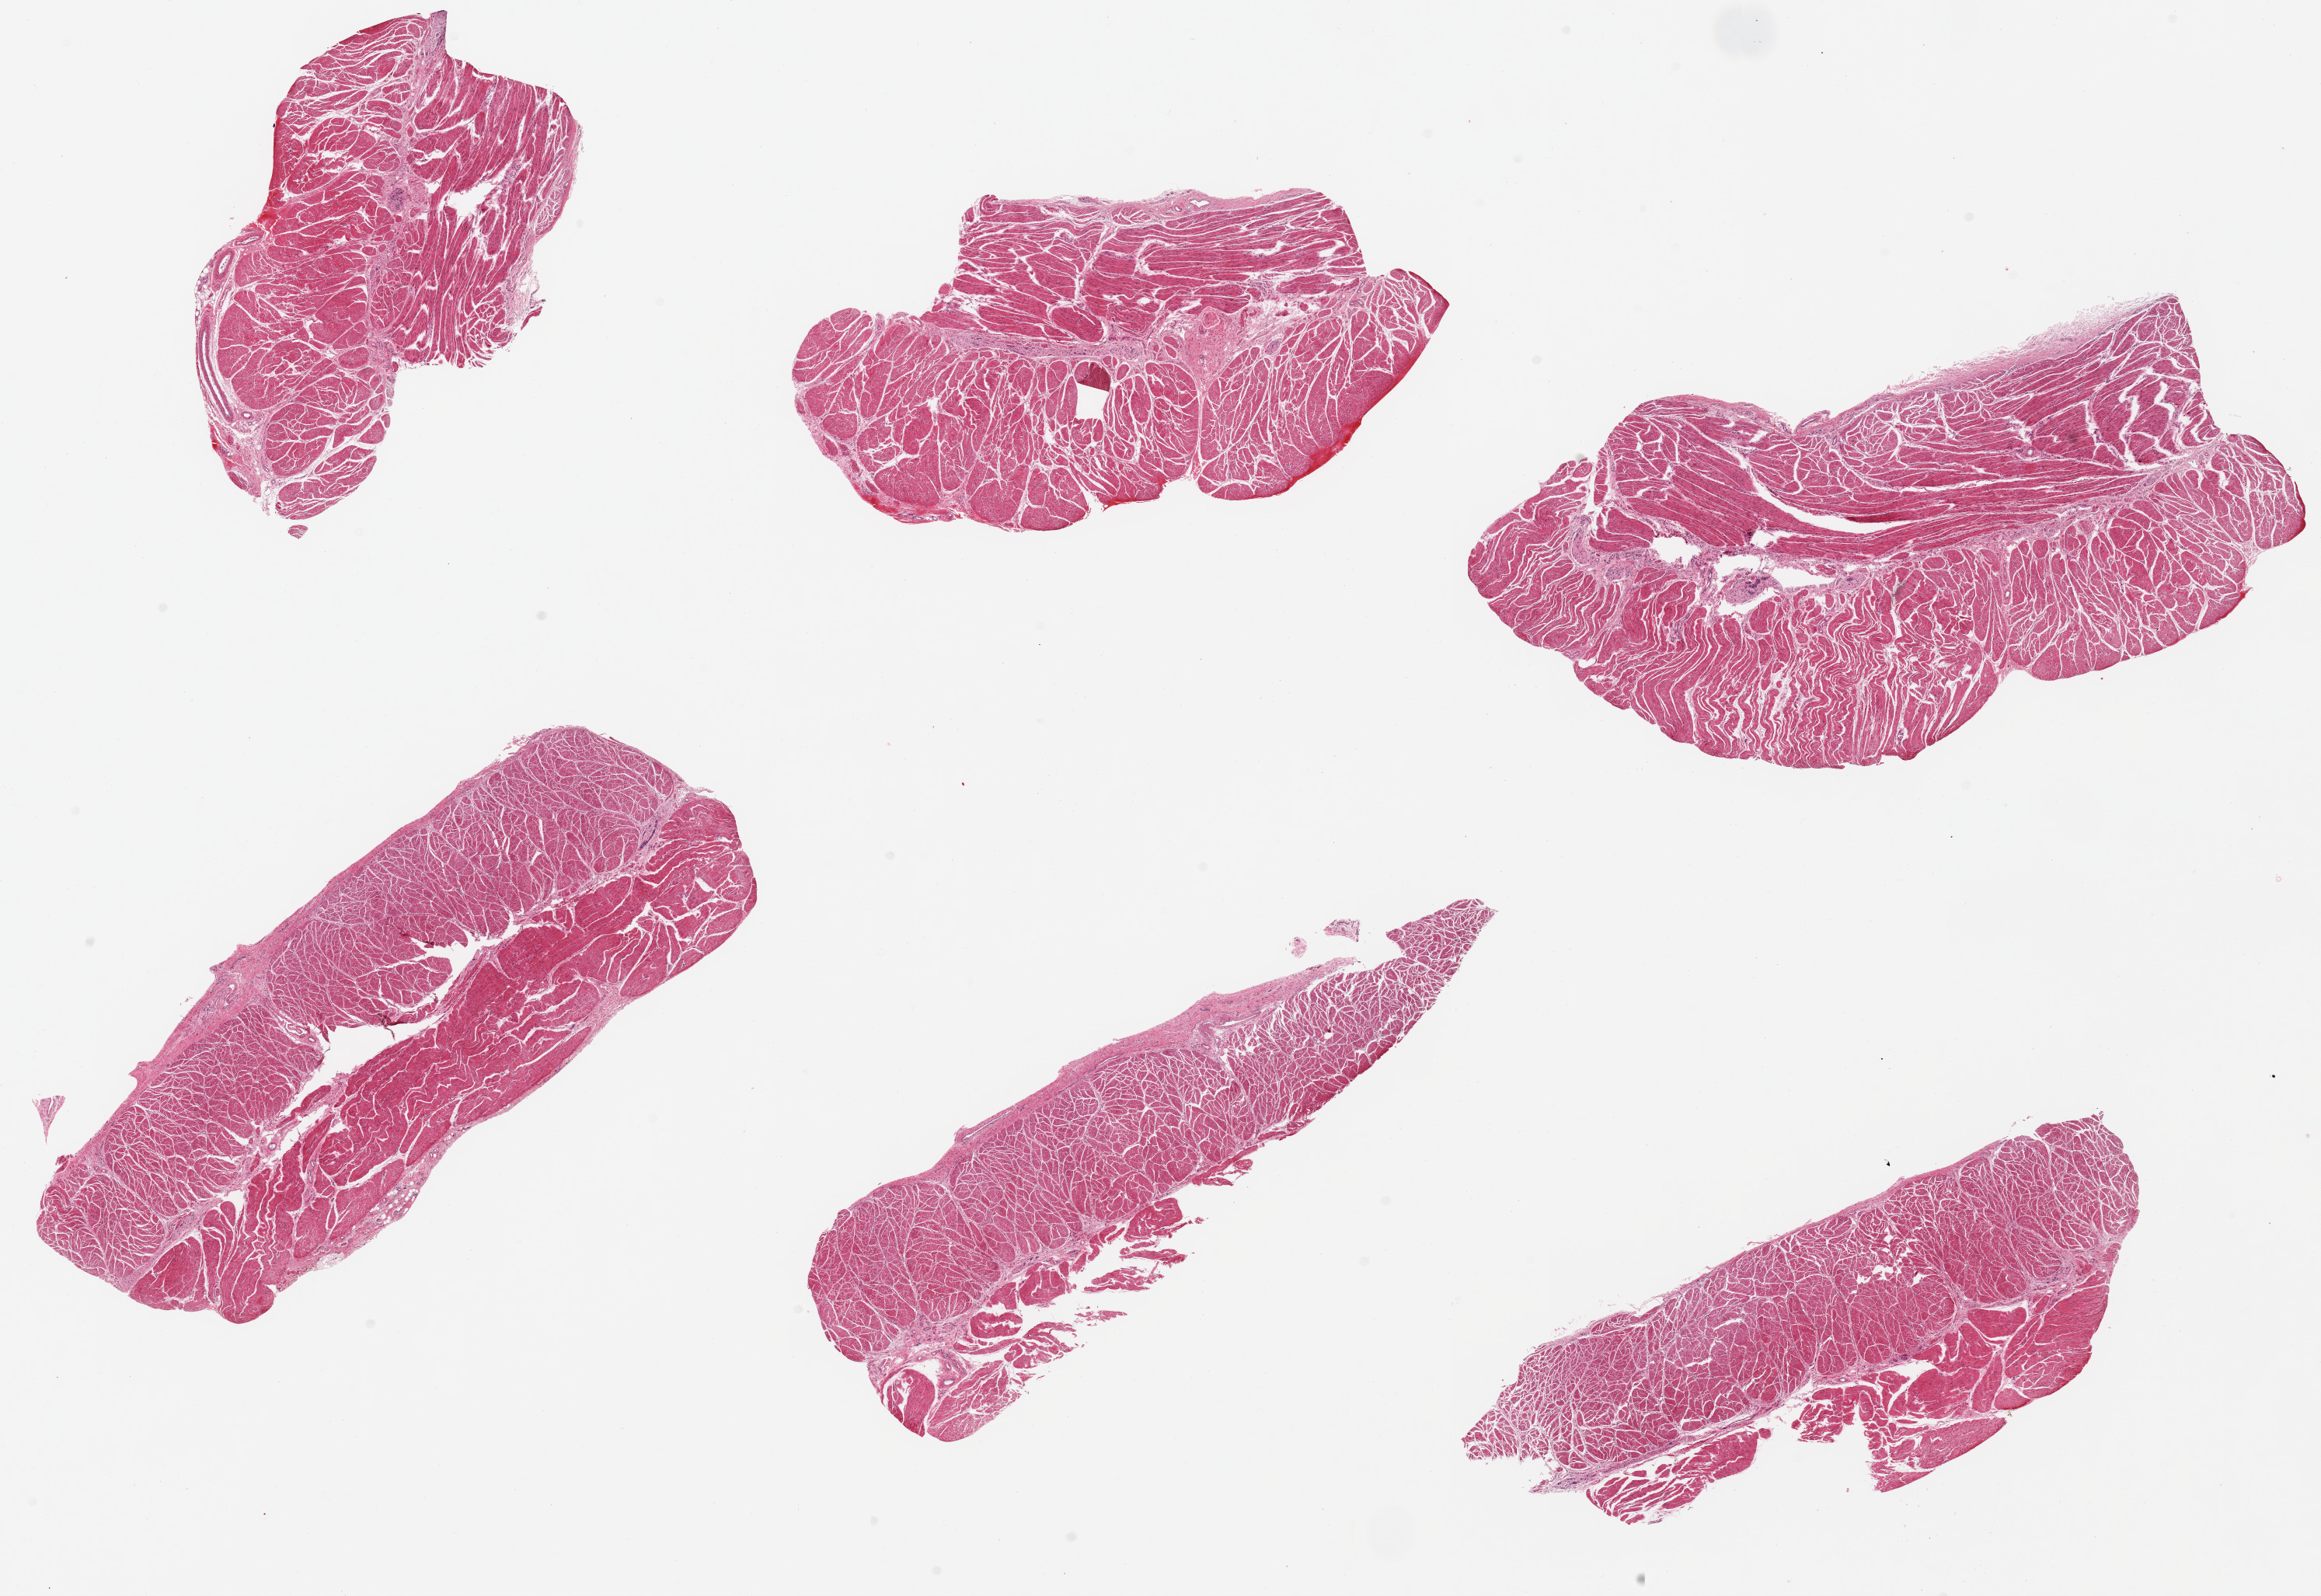
Digitized H&E-stained section, brightfield — low-resolution overview of the scanned area, about 23.6 x 16.2 mm, PAXgene-fixed paraffin-embedded (PFPE) section, target tissue: esophageal muscle, donor tissue sample. Donor sex: male.
Pathologist's review note for this sample: 6 pieces; well trimmed.